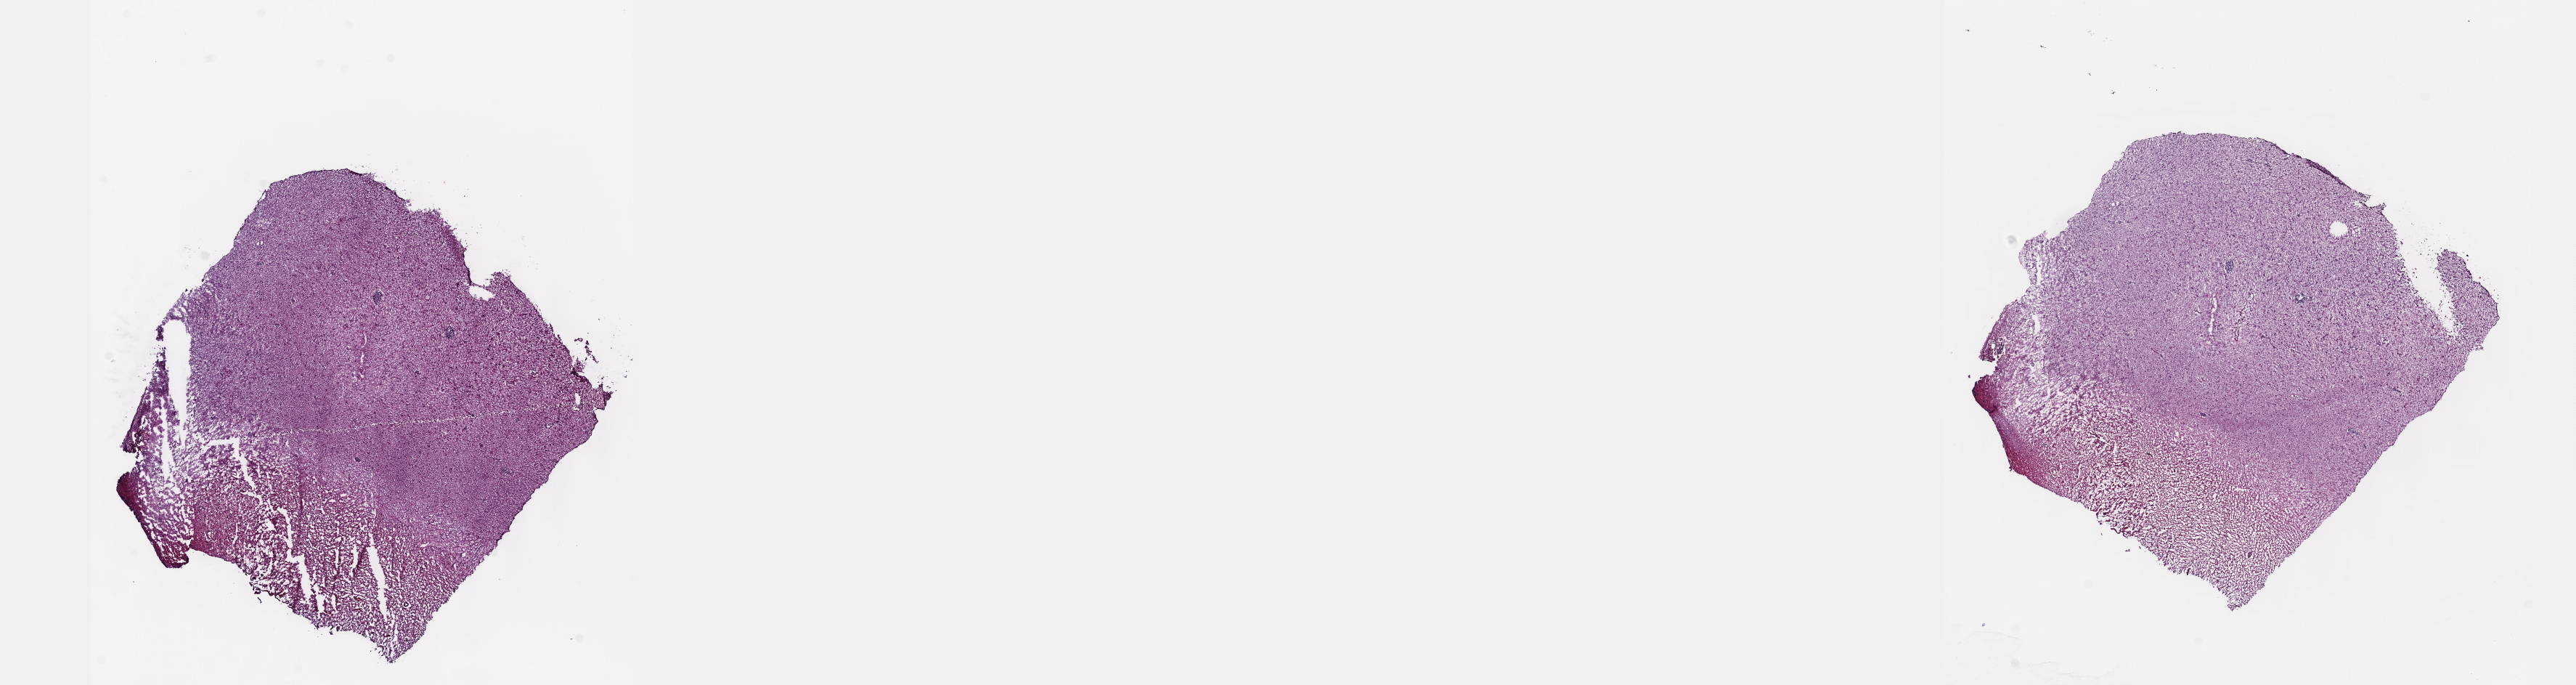
Digitized Hematoxylin and eosin (H&E) stained tissue section (whole slide) — shown as a low-resolution overview of the whole scanned area (about 28.7 x 7.6 mm, slide scanned at 40x), frozen section from the top of the tissue portion, sample: primary tumour, brain. Female patient; age at initial diagnosis 63 years. Histologic grade: G3 (poorly differentiated). Slide review estimates, as recorded: tumour cells 45%, tumour nuclei 75%, normal cells 10%, stromal cells 45%, necrosis 0%. Infiltration values recorded for this section: lymphocyte infiltration 5%, monocyte infiltration 0%, neutrophil infiltration 0%.
Histologic diagnosis: Astrocytoma, anaplastic.